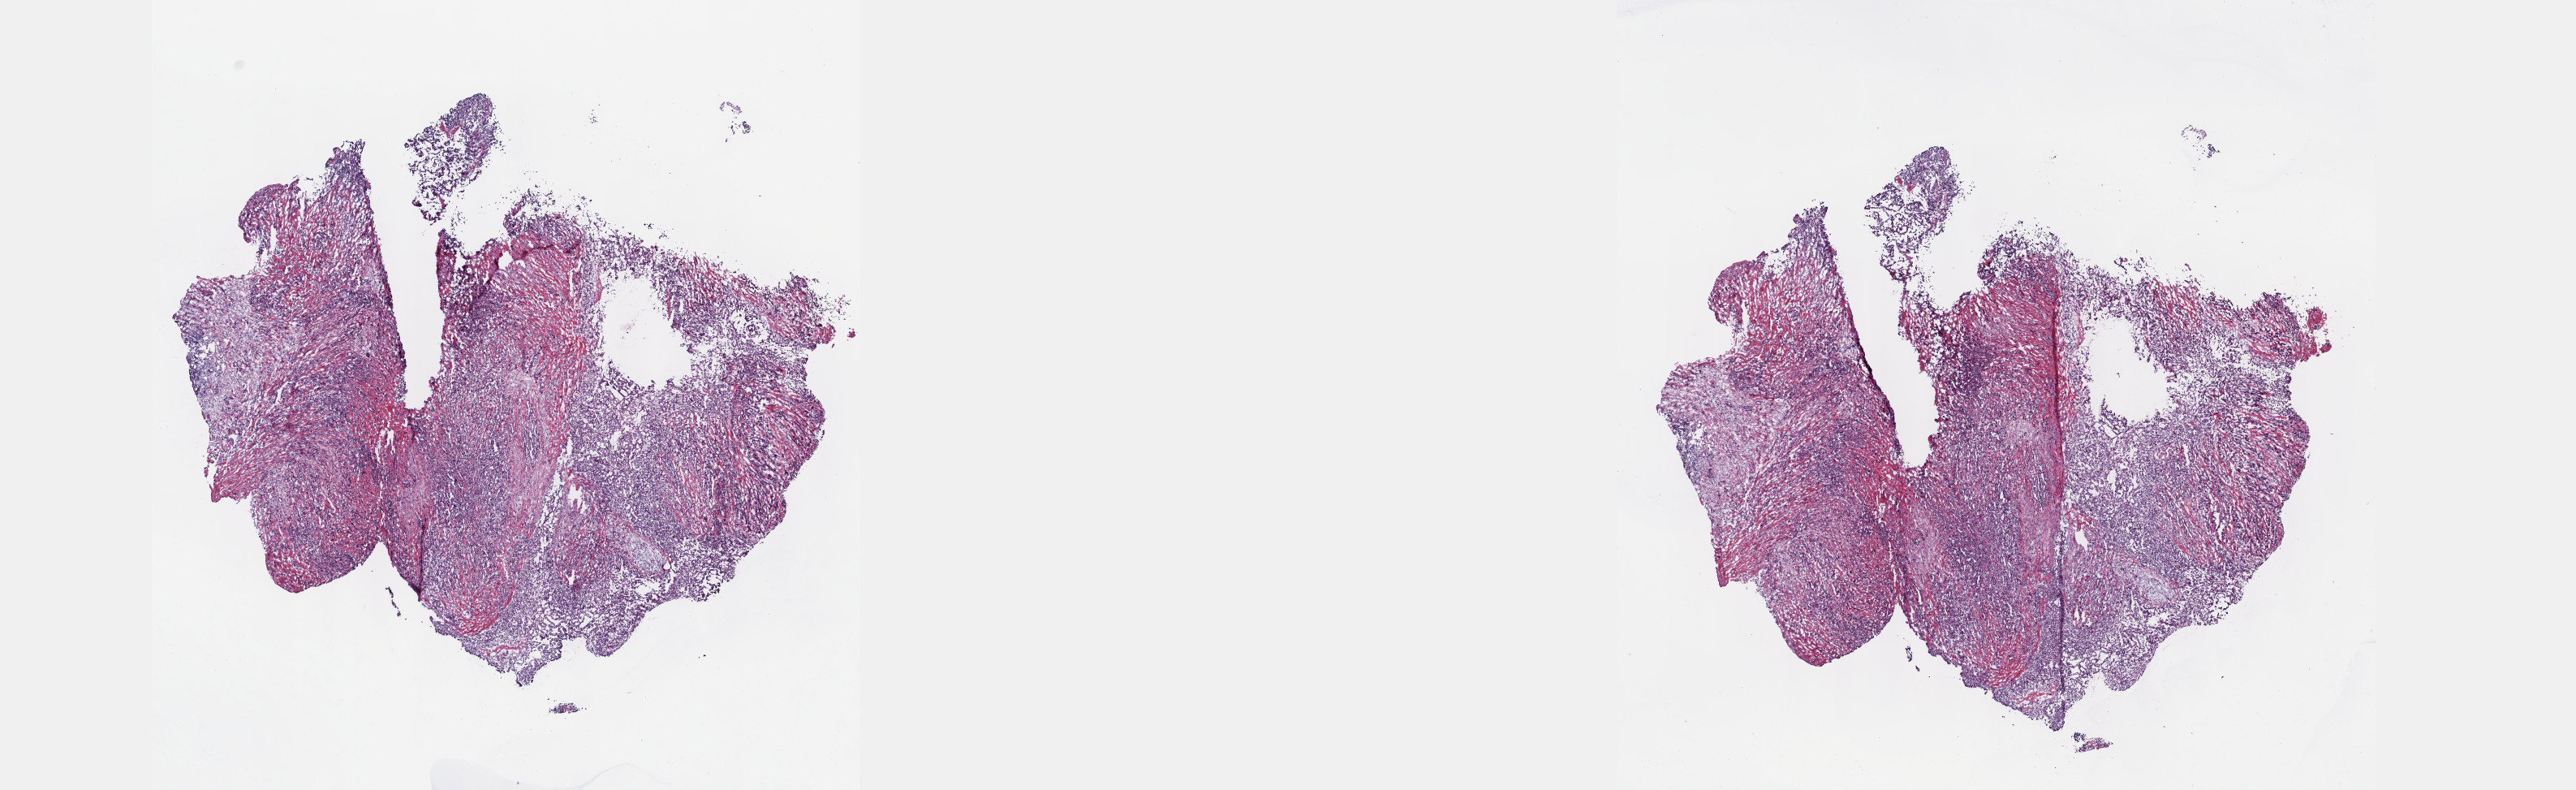
Digitized H&E tissue section (whole slide) — a low-resolution overview of the entire scanned area, about 25.7 x 7.9 mm; frozen section from the top of the tissue portion; primary tumour sample from the mesothelium. Male, age 66 years at initial diagnosis.
Histologic diagnosis: Epithelioid mesothelioma, malignant (pleura, NOS).